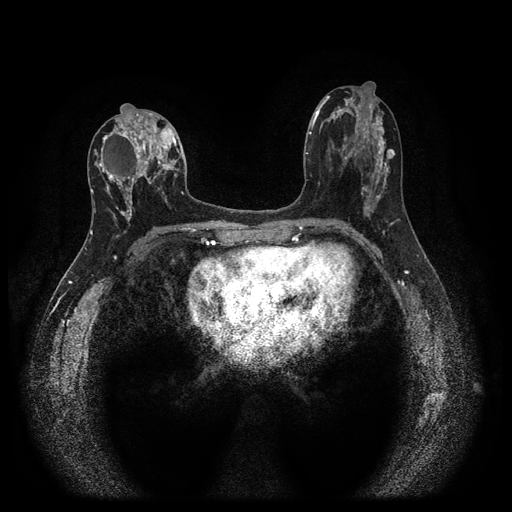
Breast MRI (dynamic contrast-enhanced, multi-phase), one axial slice. Position 50 of 116 along the scan axis. Dynamic contrast-enhanced series, time point 2 of 5 at this slice position (early post-contrast). 1.5 T. TE 2.7 ms, TR 5.4 ms. 512 × 512 image matrix, field of view 330 × 330 mm. Female patient, age 47 years.
Outlined on this slice (semi-automatically segmented with operator editing):
- breast lesion (labelled benign in the annotation): bounding box <386,149,396,161> (left, top, right, bottom; pixels)
- breast lesion (labelled 'tumour' in the annotation; benign lesions carry a separate 'benign' label): <93,114,178,229>